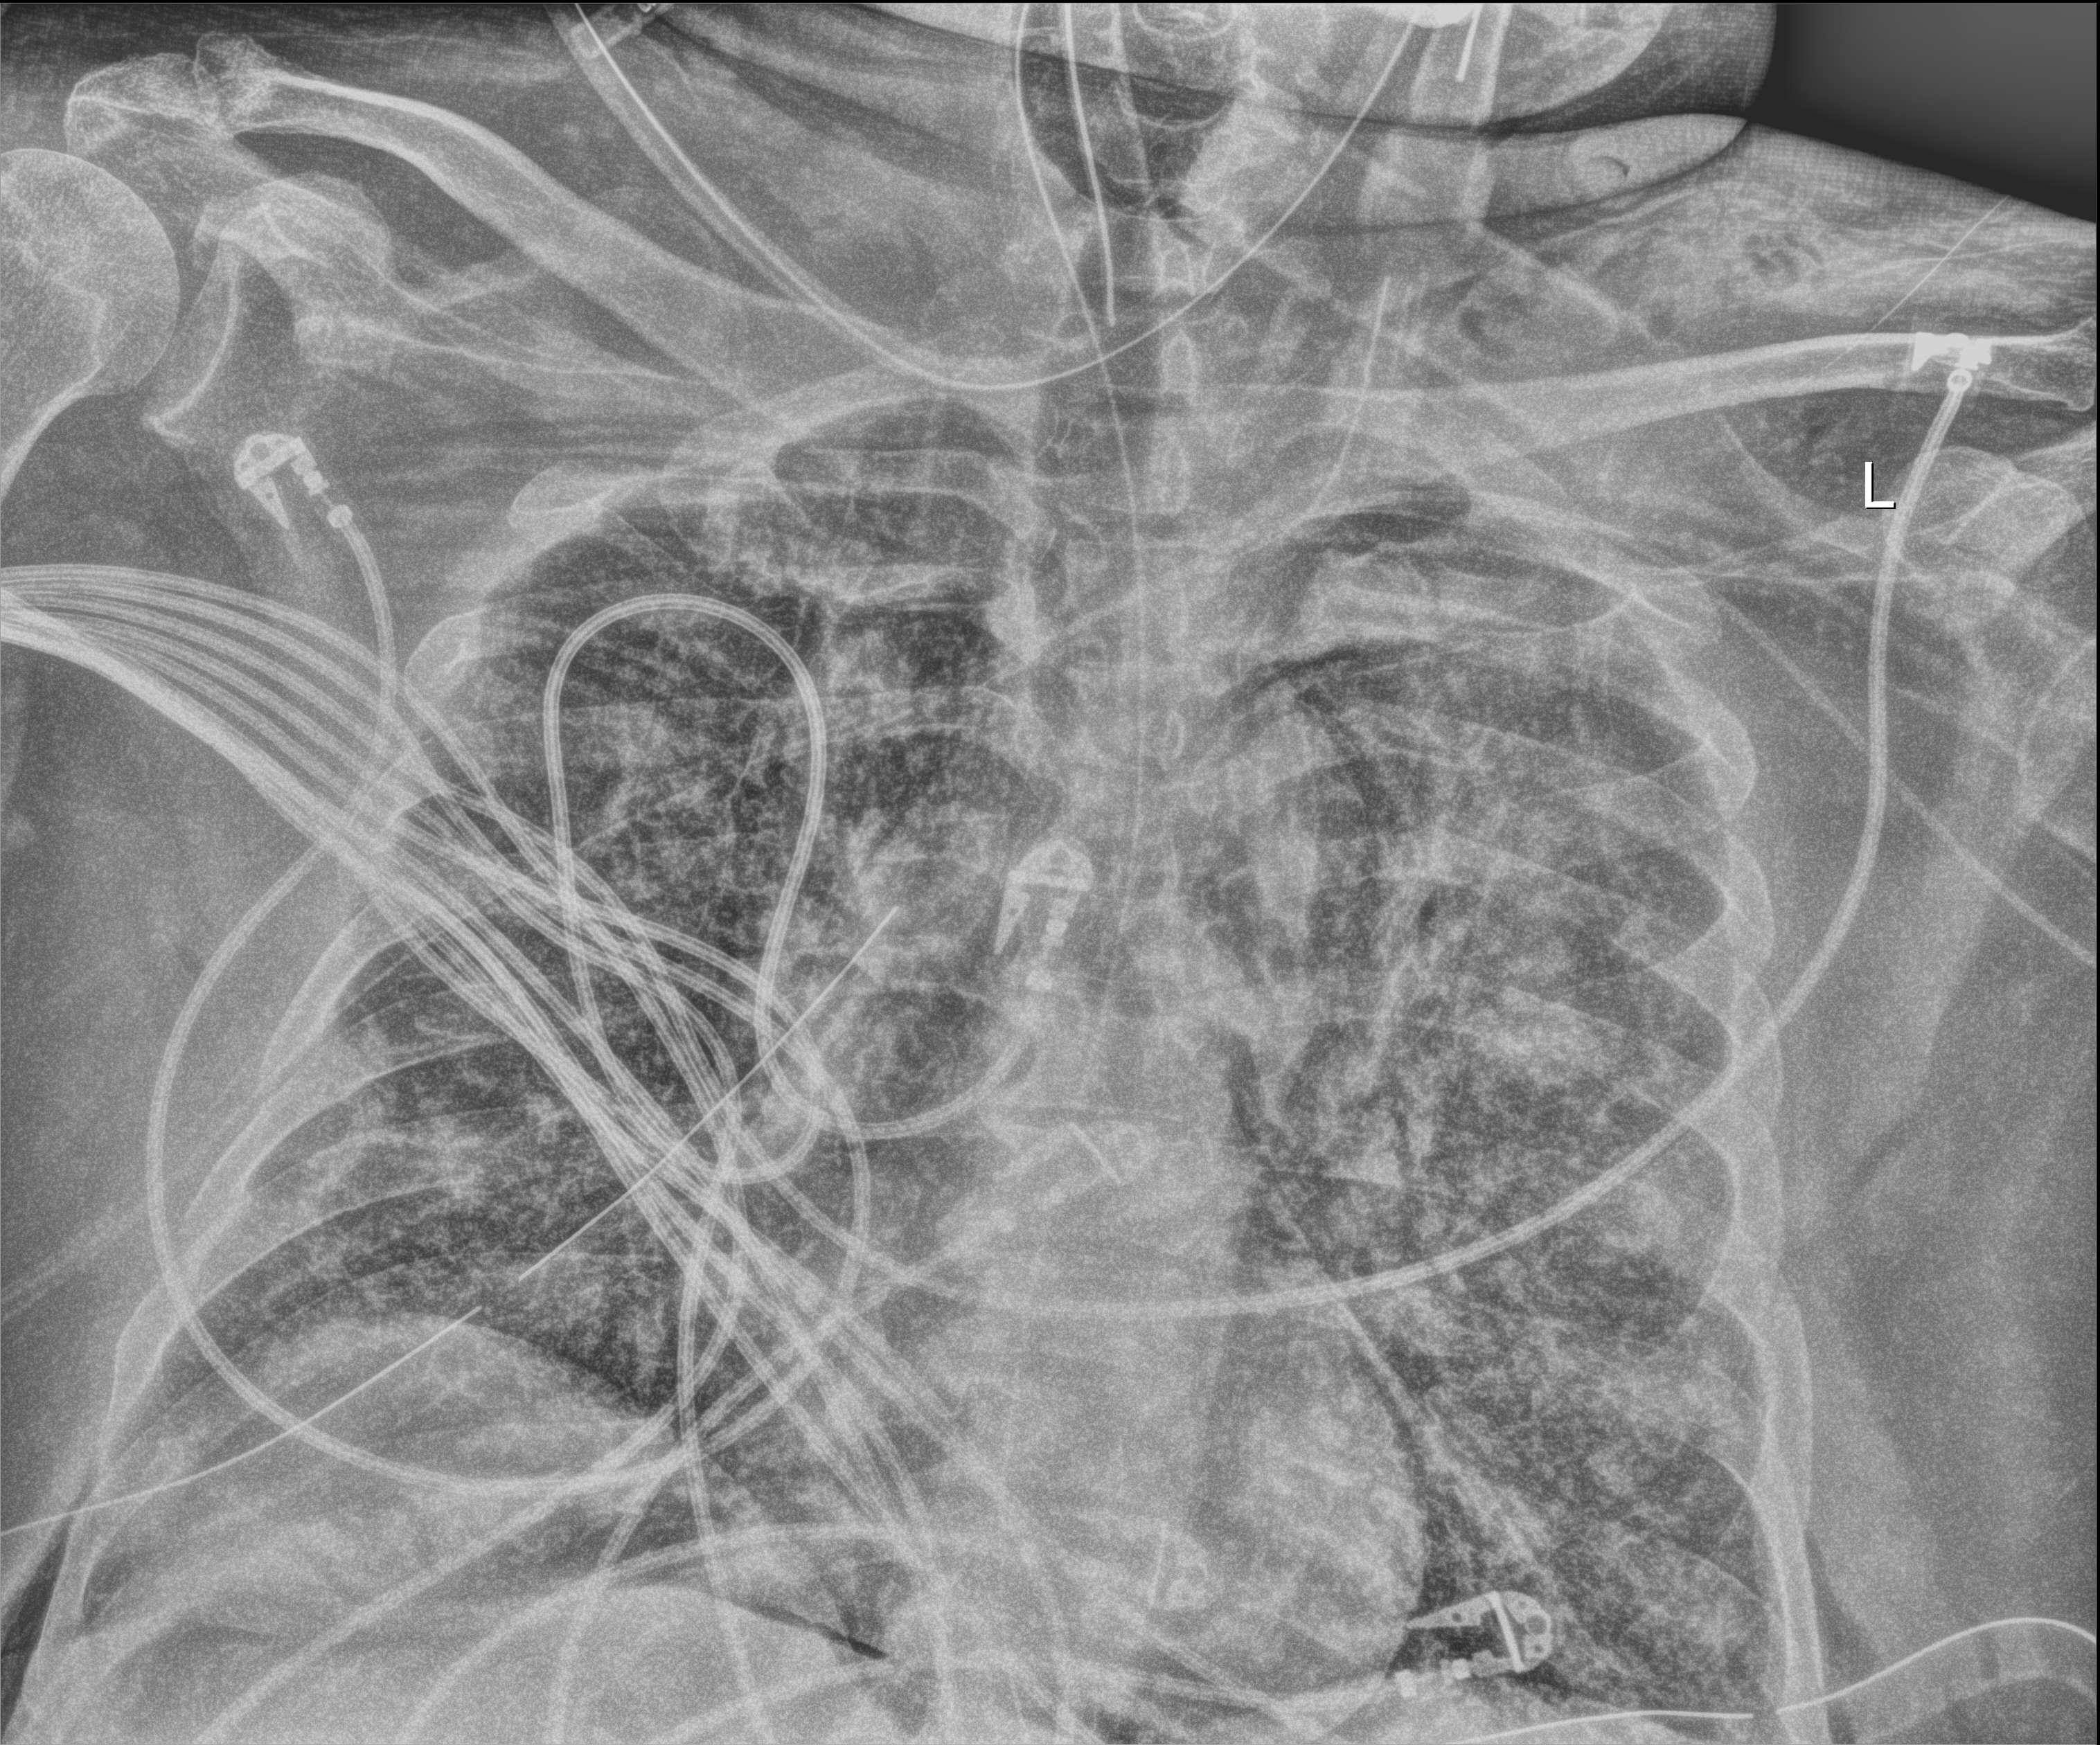
Bedside chest radiograph (digital radiography); anteroposterior (AP) projection. Patient hospitalised with COVID-19, aged 18–59 years.
Hospital-stay facts (about this admission, not read from this image; timing relative to this image not recorded): admitted to intensive care during this hospital stay: yes; mechanically ventilated during this hospital stay: yes.